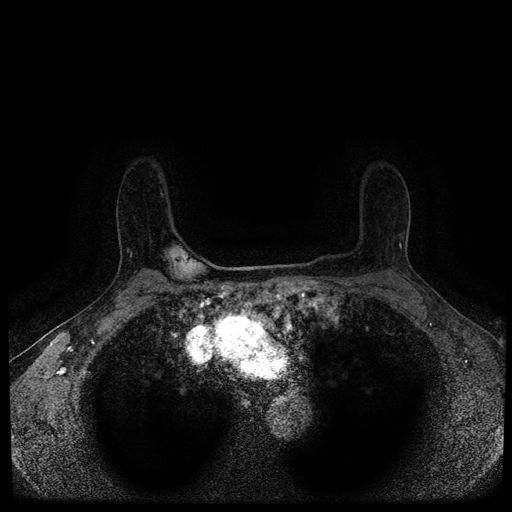
Breast MRI (dynamic contrast-enhanced, multi-phase), one axial slice; position 78 of 116 along the scan axis; dynamic contrast-enhanced series, time point 2 of 5 at this slice position (early post-contrast); 1.5 T; TE 2.7 ms, TR 5.4 ms; 512 × 512 image matrix, field of view 330 × 330 mm. Female patient, age 63 years.
Annotated regions visible in this slice (semi-automatically segmented with operator editing):
- breast lesion (labelled 'tumour' in the annotation; benign lesions carry a separate 'benign' label): bounding box <160,255,165,261> (left, top, right, bottom; pixels)